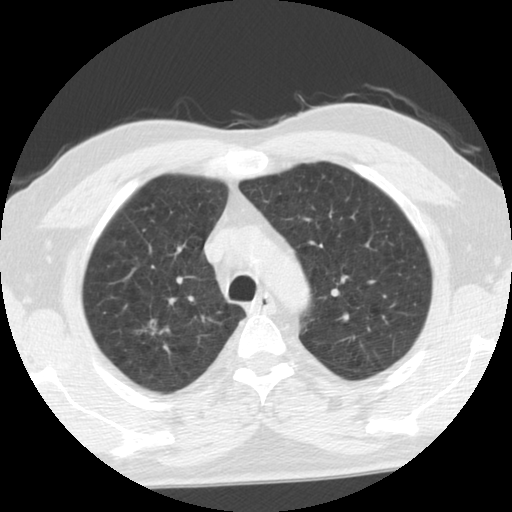
Chest CT (low-dose screening protocol), one axial image. Second screening round (one year after baseline). Lung window (W 1500 / L -600 HU). 2.5 mm slice thickness. 512 × 512 image matrix, field of view 330 × 330 mm. Male, age 68 years at enrolment. Former smoker at enrolment.
Expert-annotated lung lesion, bounding box <130,312,173,348> (left, top, right, bottom; pixels). The exam's reader record, not a measurement of the box and not confirmed to be the same lesion: non-calcified nodule or mass ≥4 mm, right upper lobe, poorly defined margins, ground glass attenuation, pre-existing on the prior screen: yes; interval growth: yes. Official screen result: positive, other. Later outcome: lung cancer diagnosed 88 days after this screen — adenocarcinoma, NOS, right upper lobe, moderately differentiated (G2), stage IA (AJCC 6th edition), 28 mm at pathology.